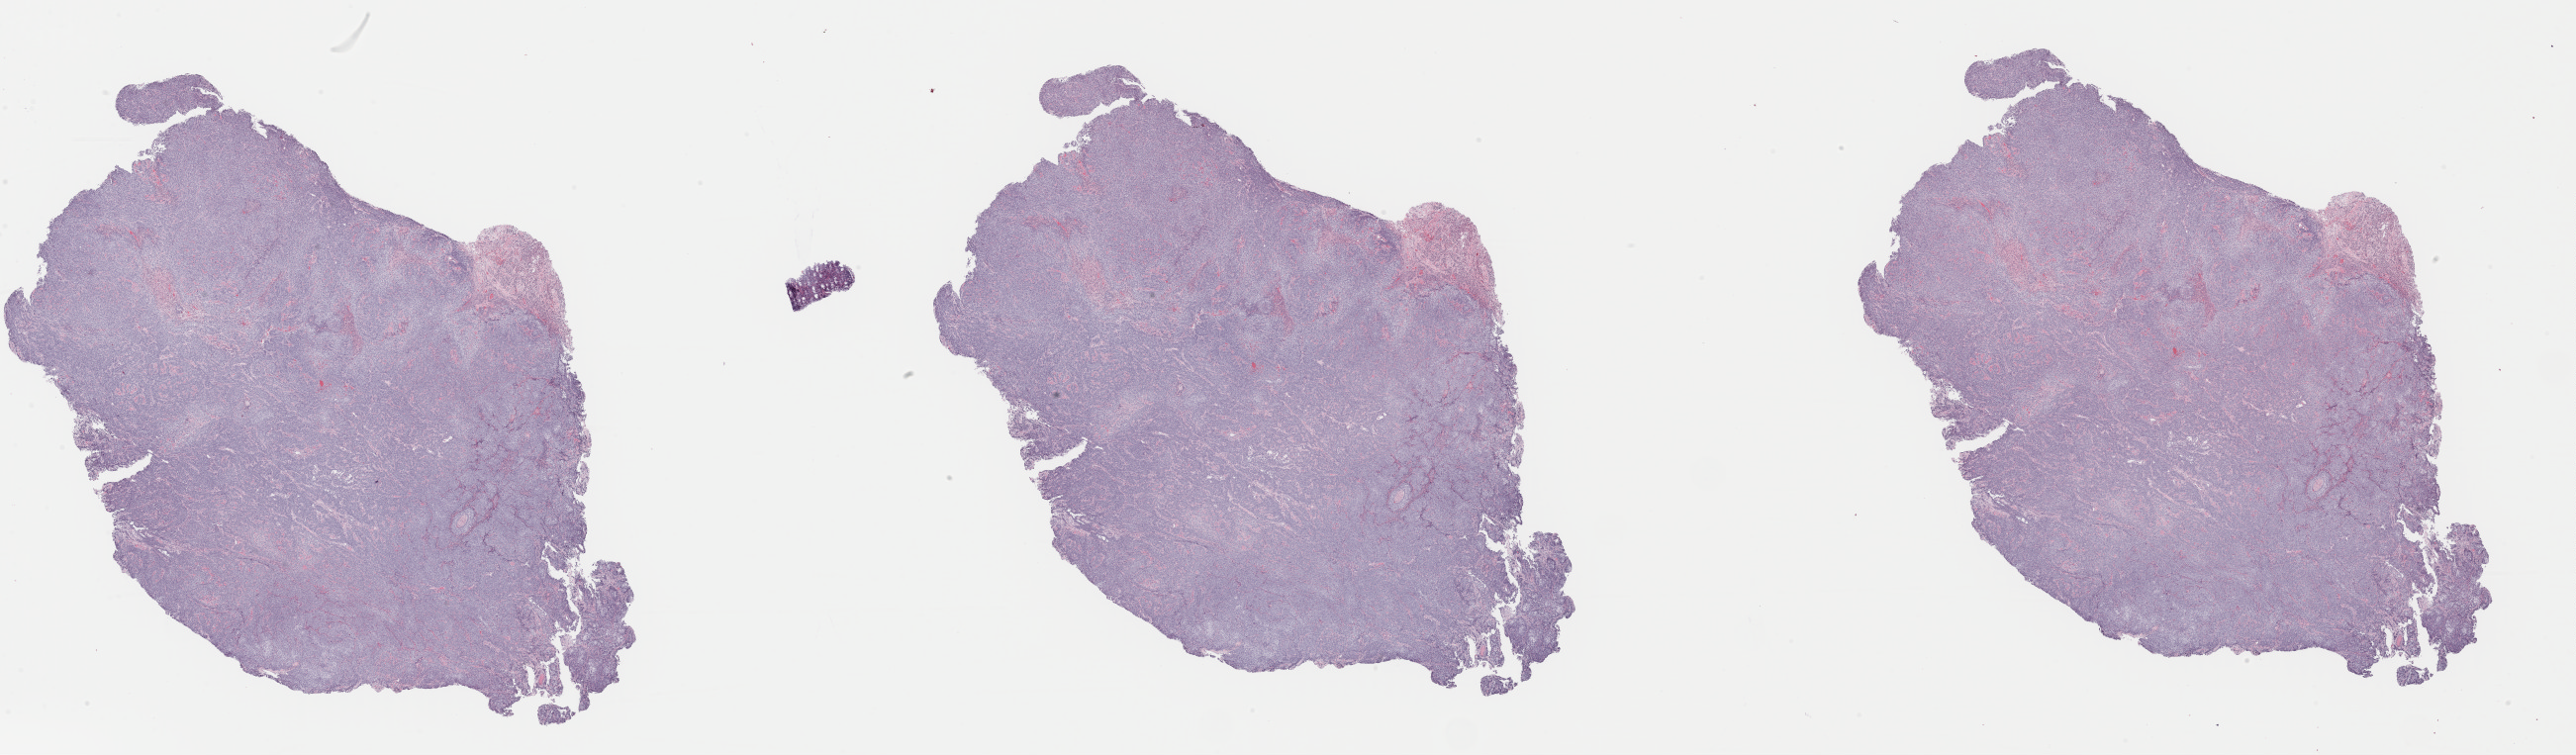
Digitized H&E-stained tissue section (whole slide) — a low-resolution overview of the entire scanned area, about 41.1 x 12.0 mm (acquisition: 40x scan), formalin-fixed paraffin-embedded (FFPE) diagnostic section, primary tumour sample from the head and neck. Male, age 57 years at initial diagnosis.
Histologic diagnosis: Squamous cell carcinoma, NOS (tongue, NOS).